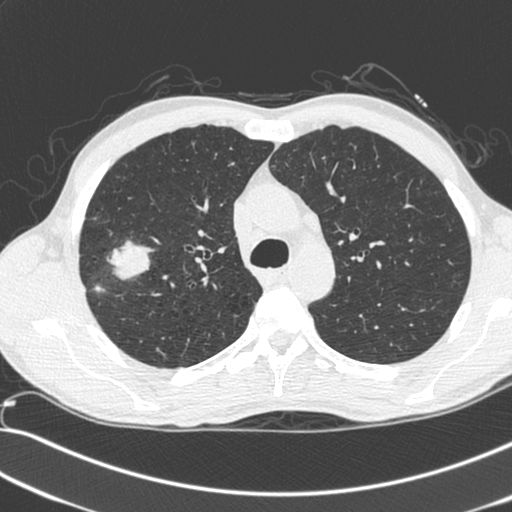
Axial slice from a low-dose chest CT screening exam, first (baseline) screen, lung window (W 1500 / L -600 HU), slice 72 of 281 in the series, 512 × 512 image matrix, field of view 341 × 341 mm. Male participant, aged 55 years at enrolment.
• Expert-annotated lung lesion, box from (x=72, y=236) to (x=150, y=308) px.
• Reader record for this screening exam (exam-level; its link to the box is not recorded): non-calcified nodule or mass ≥4 mm, right upper lobe, 52 × 39 mm, spiculated (stellate) margins, soft tissue attenuation.